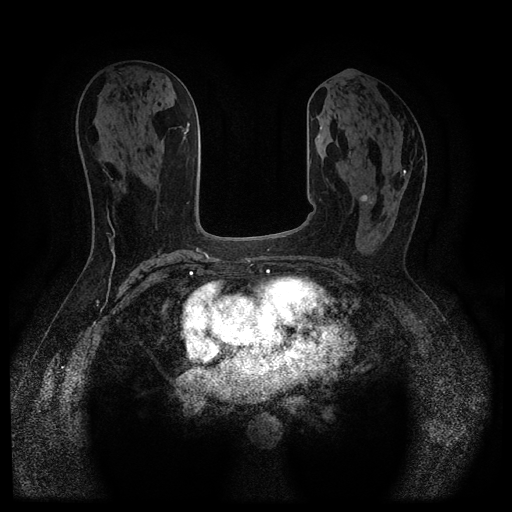
Breast MRI (dynamic contrast-enhanced, multi-phase), one axial slice; slice 50 of 116 in the series (ordered by position); dynamic contrast-enhanced series, time point 2 of 5 at this slice position (early post-contrast); 1.5 T; TE 2.6 ms, TR 5.4 ms; 512 × 512 image matrix, field of view 340 × 340 mm. Female patient, age 64 years.
Structures marked on this image (semi-automatic segmentation, software-assisted and operator-edited):
- breast lesion (labelled 'tumour' in the annotation; benign lesions carry a separate 'benign' label): box from (x=360, y=194) to (x=374, y=205) px